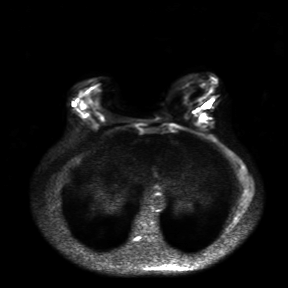
Breast MRI, one axial slice. Slice 7 of 30 in the series (ordered by position). Diffusion-weighted series; image 2 of 4 stored at this slice position (different b-values; order by instance number). 3 T. 4 mm slice thickness. 288 × 288 image matrix, field of view 360 × 360 mm. Female patient.
Structures marked on this image (outlined manually by an expert reader):
- tumour on diffusion-weighted imaging: box from (x=193, y=109) to (x=209, y=120) px